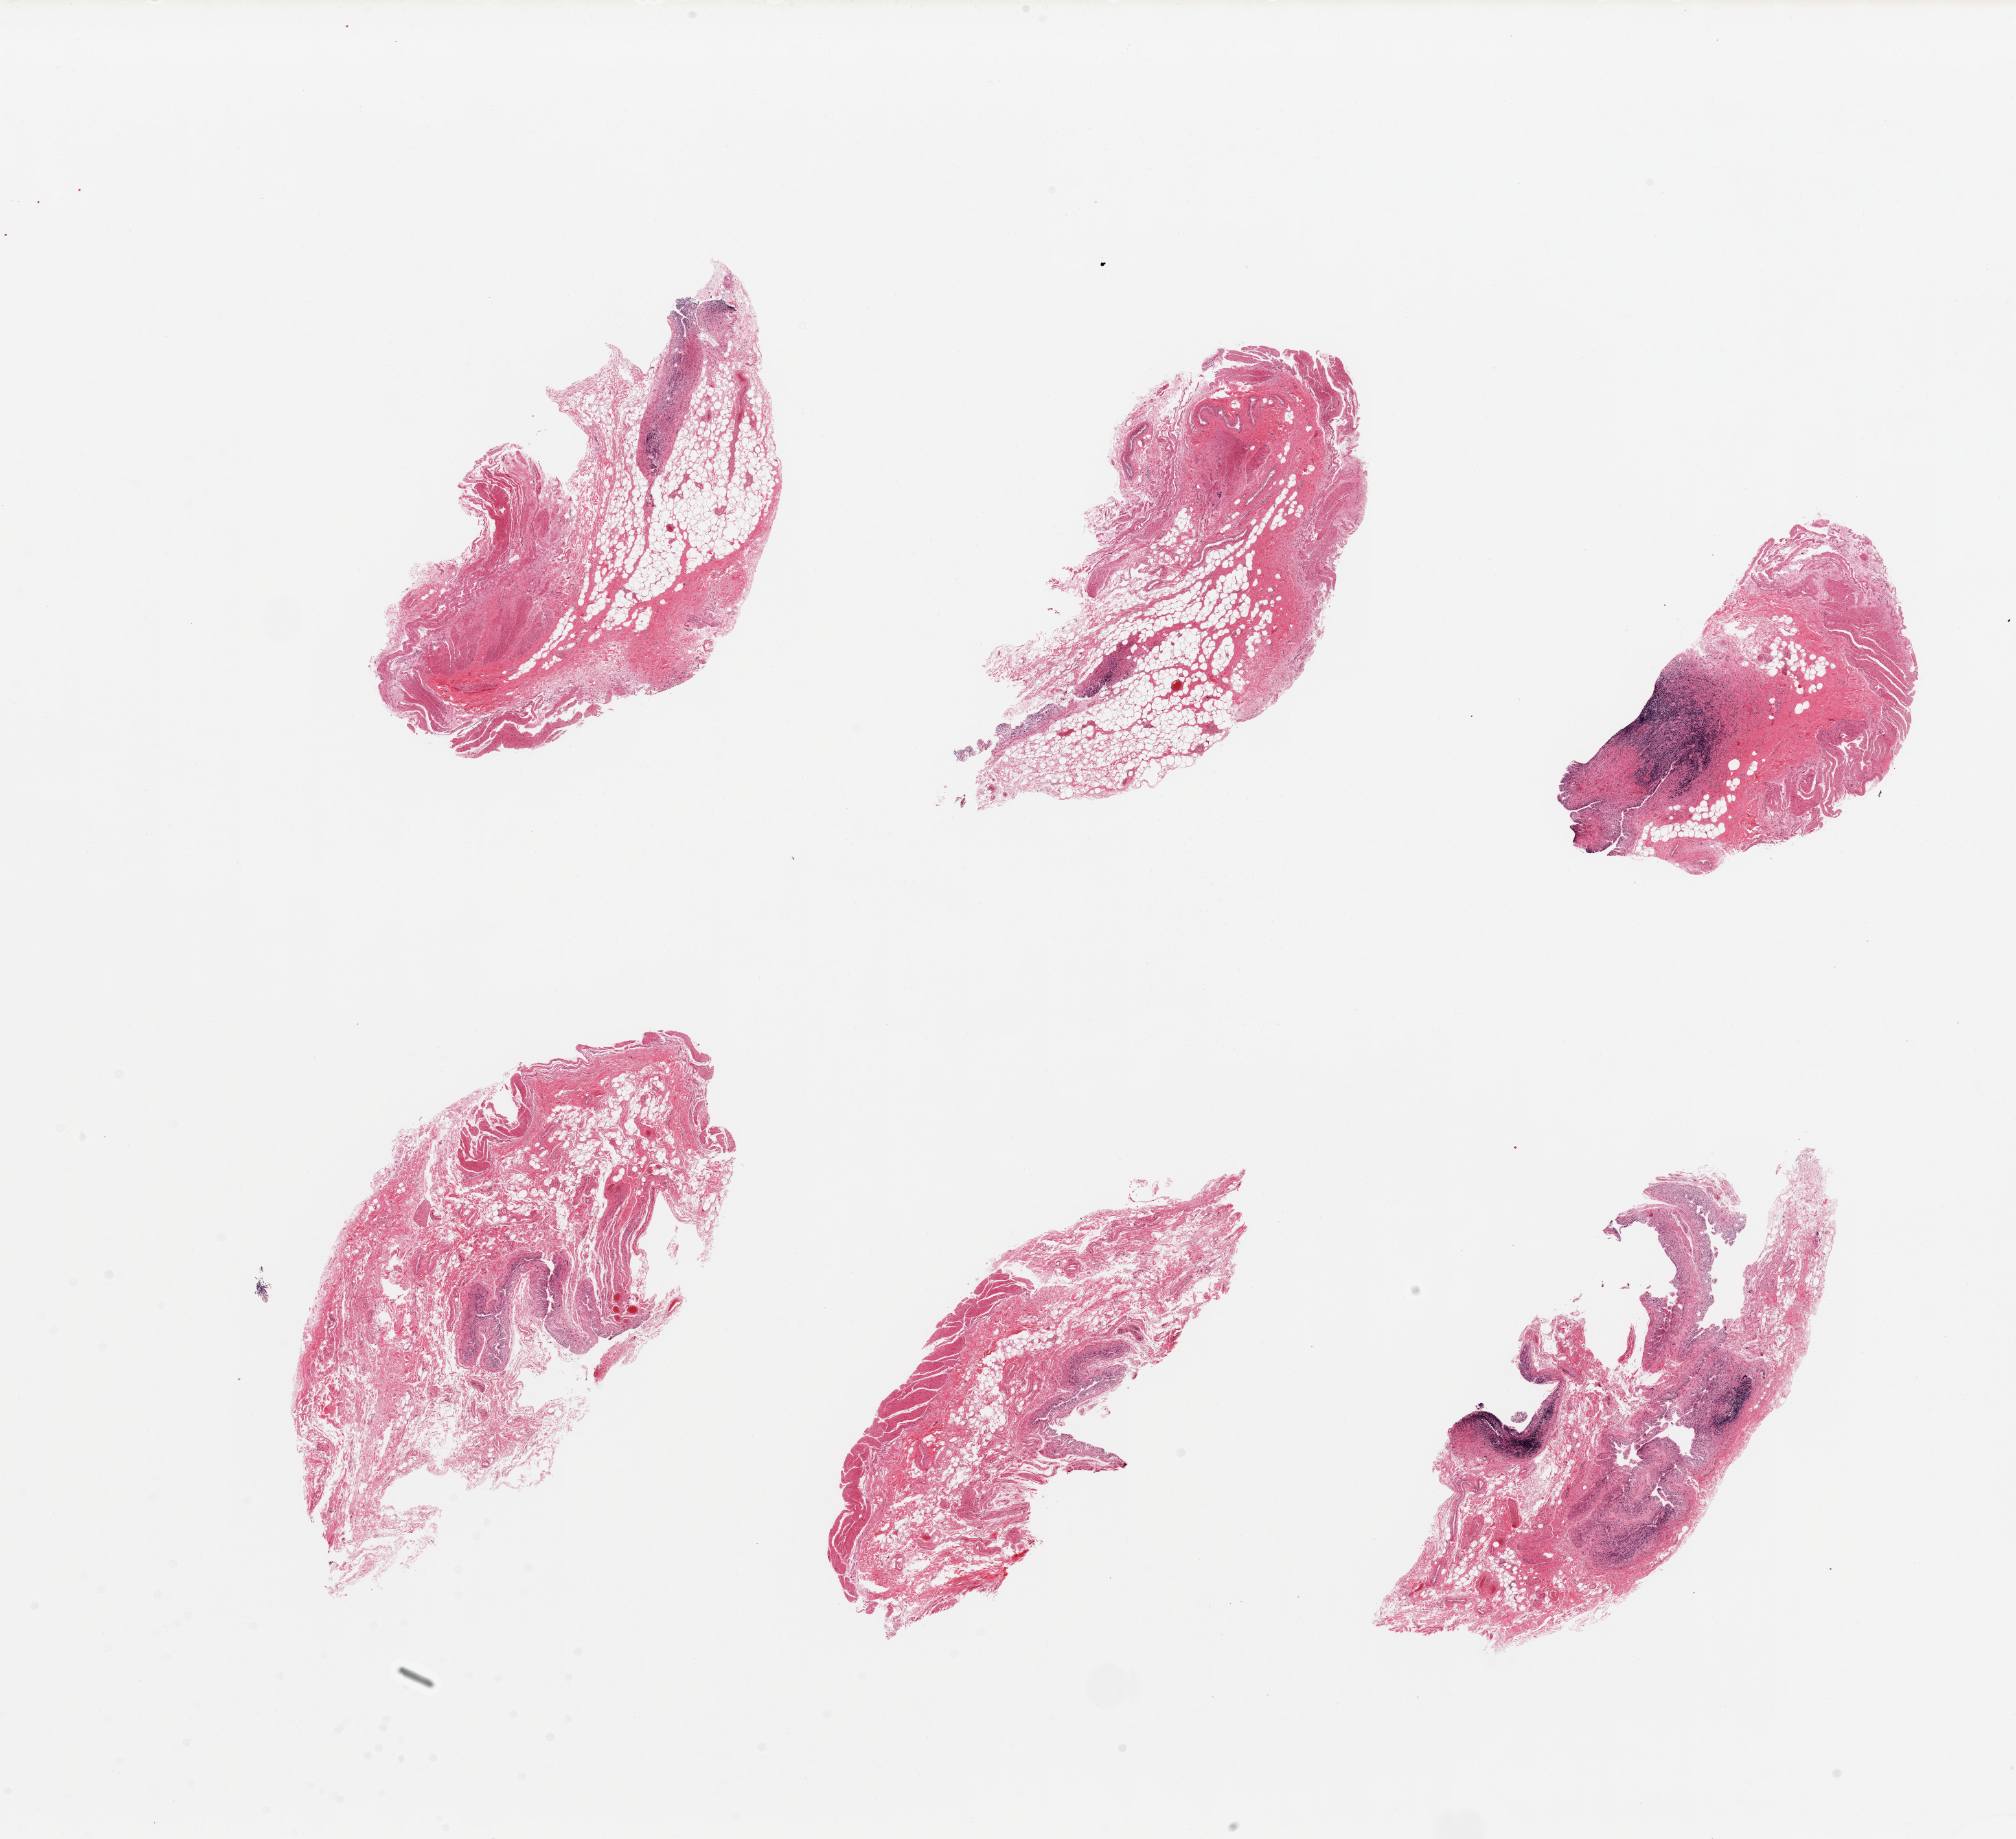
Hematoxylin and eosin (H&E) whole-slide image — shown as a low-resolution overview of the whole scanned area (about 24.6 x 22.5 mm, from a 20x scan).
* specimen: PAXgene-fixed paraffin-embedded (PFPE) section; target tissue: ileum; tissue donor sample